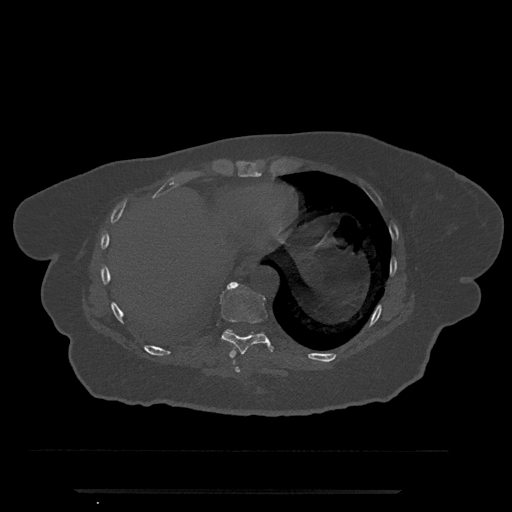
CT including the spine, one axial slice; slice 331 of 797 in the series (ordered by position); 120 kVp; bone window (W 1800 / L 400 HU); 512 × 512 image matrix, field of view 440 × 440 mm. Female patient, age 51 years. Case-level facts recorded for this patient, not image findings: primary cancer: neuro.
Outlined on this slice (semi-automatic segmentation, software-assisted and operator-edited):
- T10 vertebra: box from (x=227, y=330) to (x=231, y=332) px
- T8 vertebra: (x=234, y=364)–(x=240, y=373)
- T9 vertebra: (x=208, y=282)–(x=274, y=358)